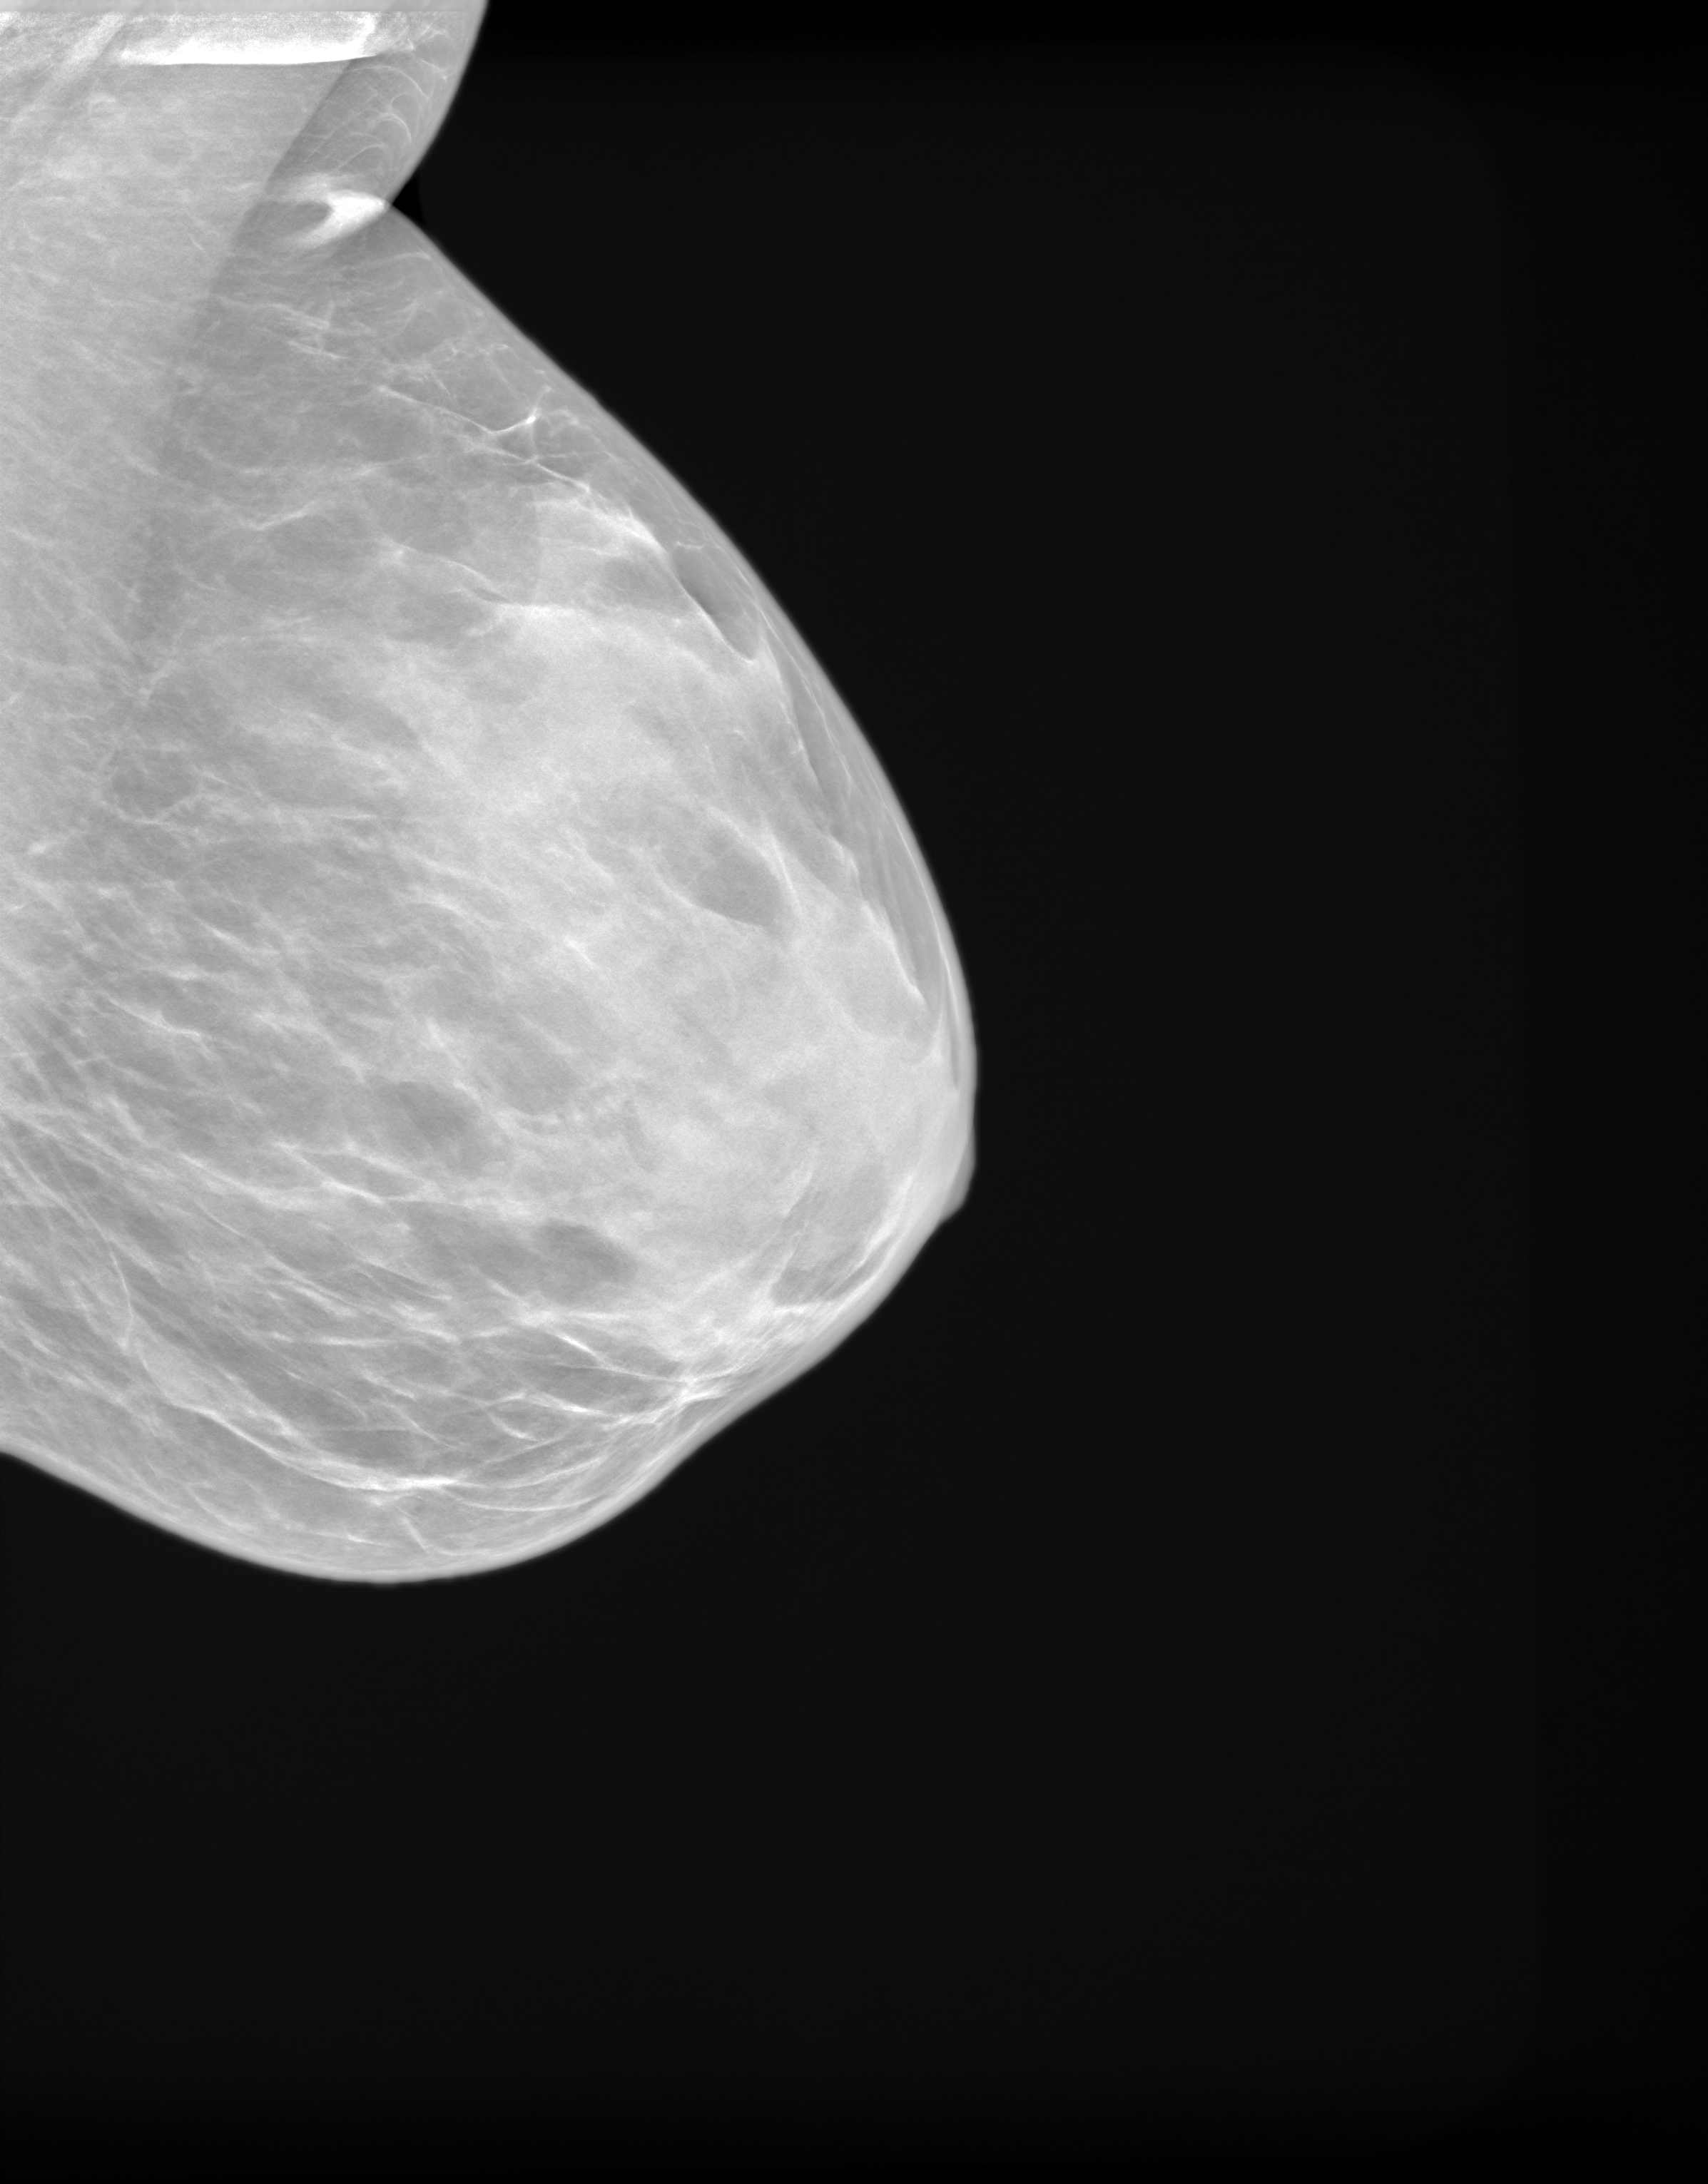
Screening examination, system: SenoIris_1SP1.1(421). Patient aged 48 years (female).
Image type: synthesized 2-D view from tomosynthesis. Breast: left. Projection: MLO view.